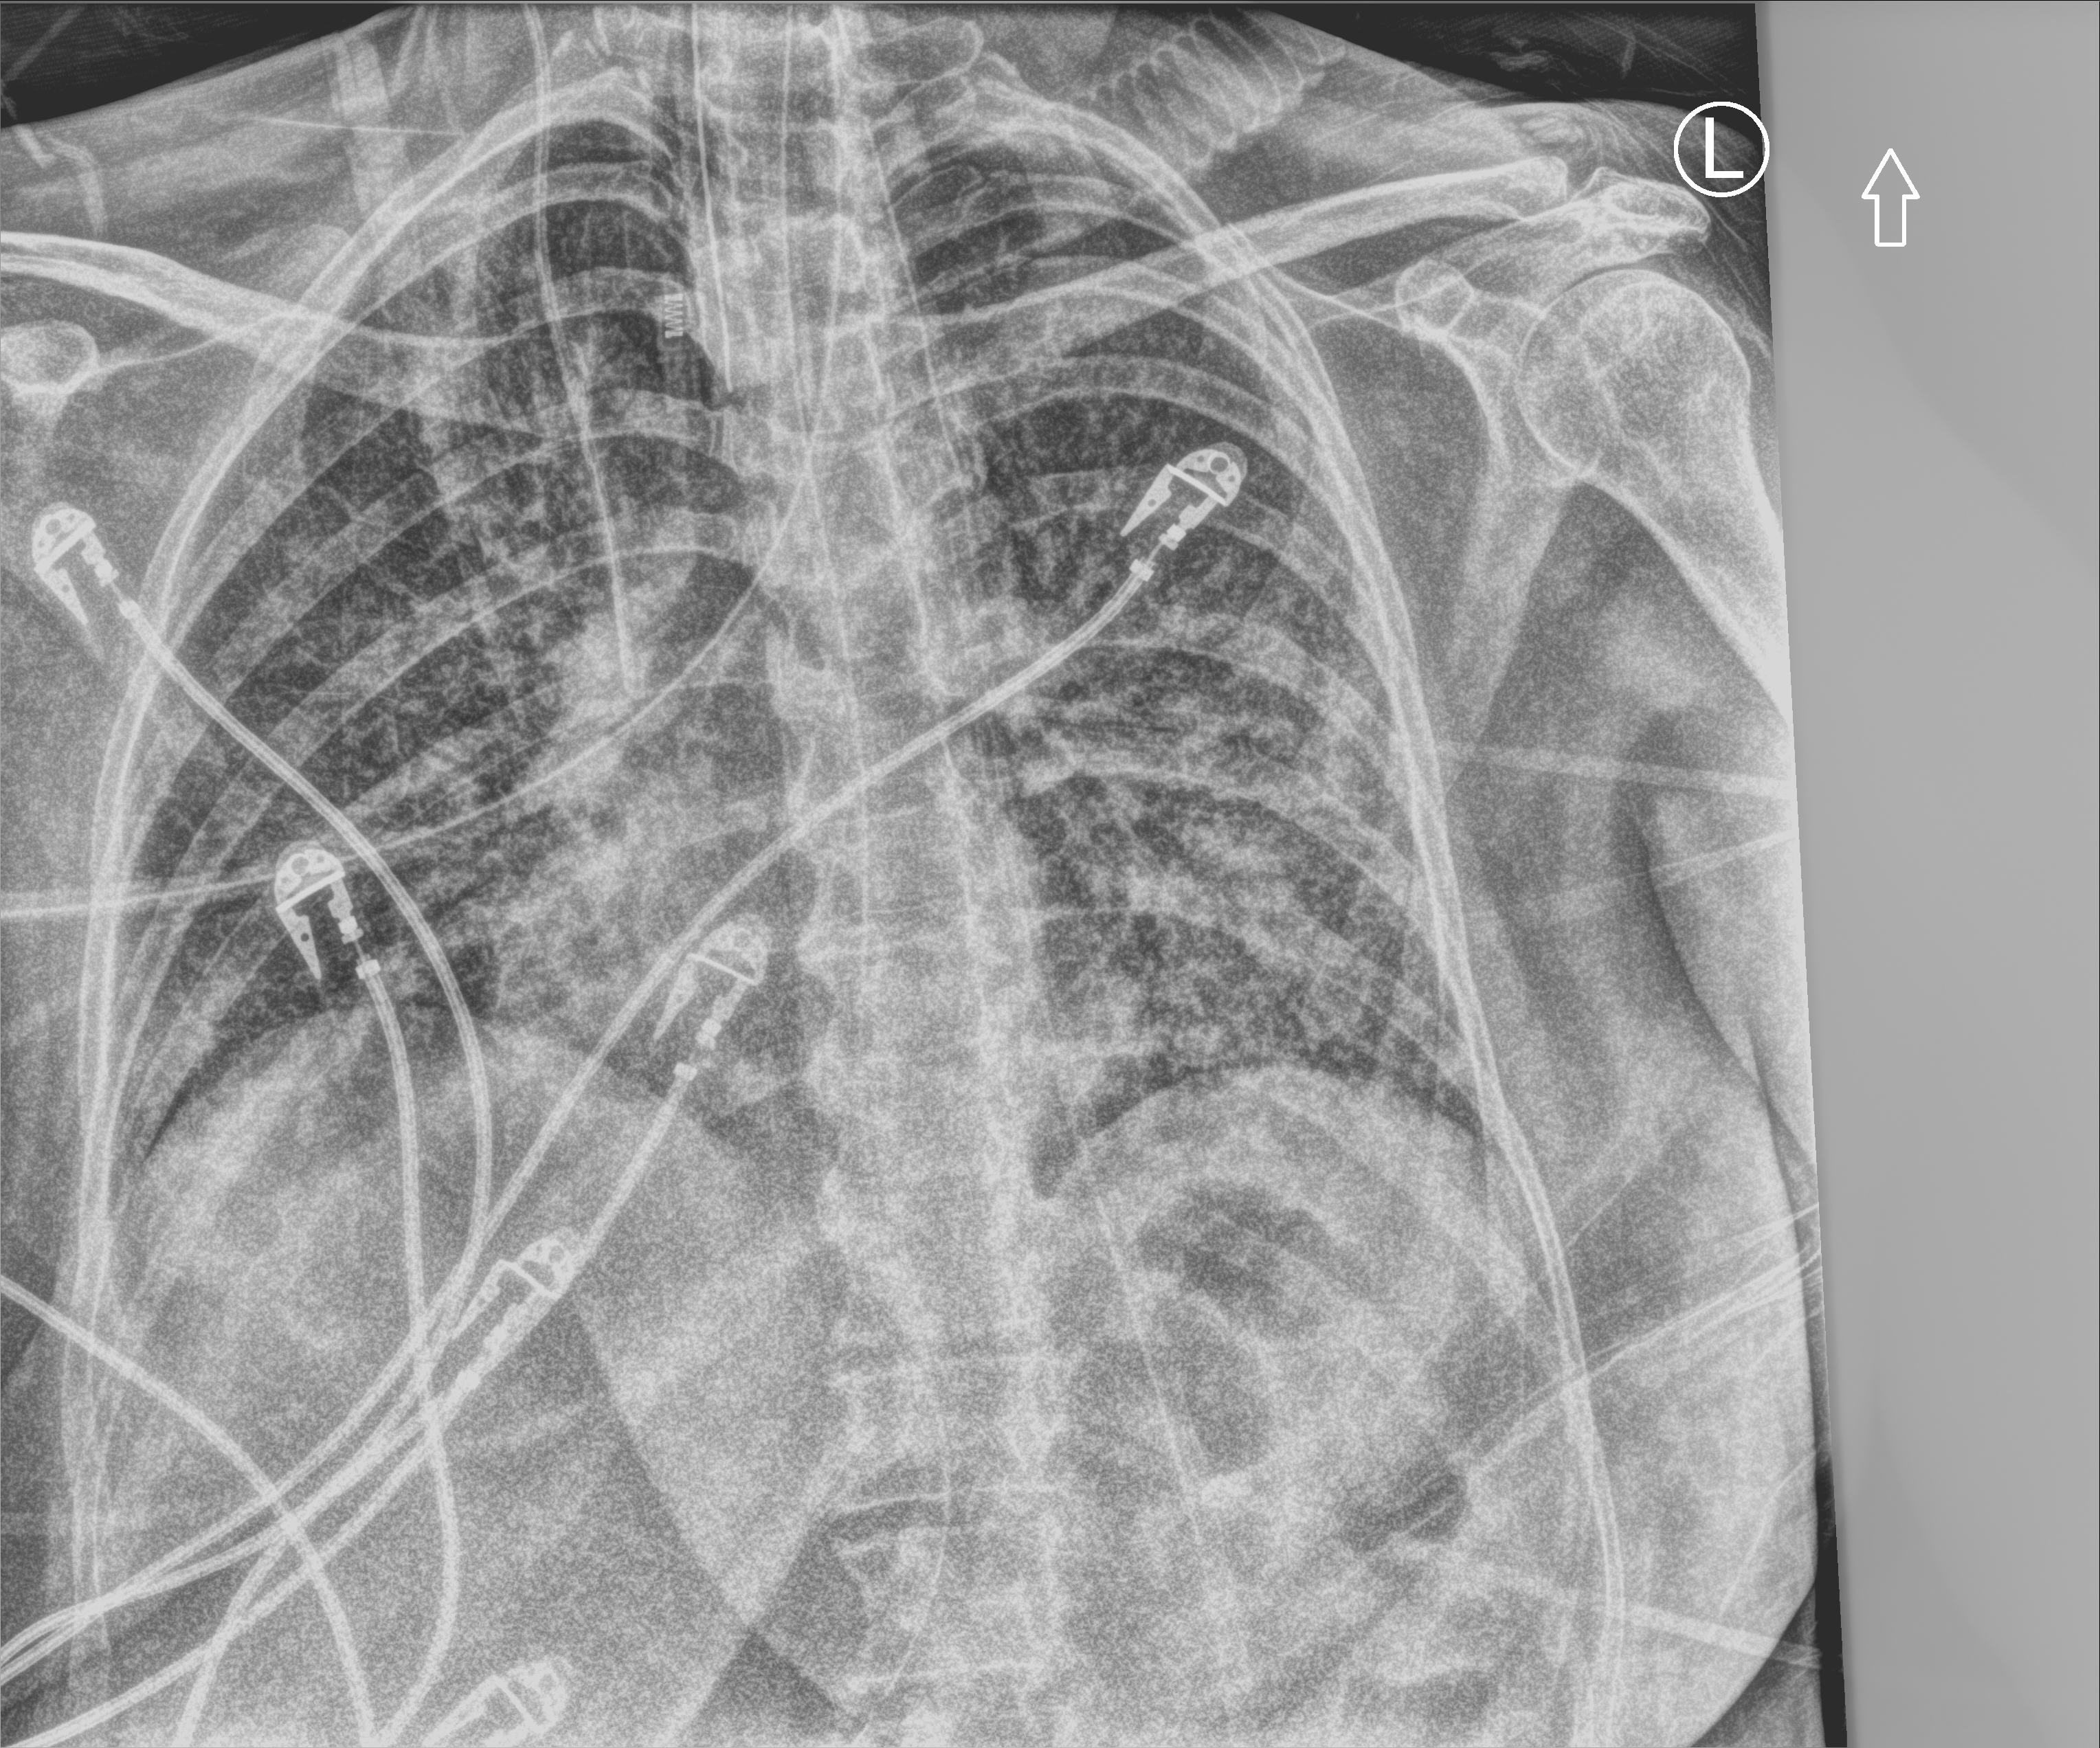
Bedside chest radiograph (computed radiography), anteroposterior (AP) projection. Patient hospitalised with COVID-19; female, aged 60–74 years.
Admission-level facts for this patient (not findings on this image; timing relative to this image not recorded): admitted to intensive care during this hospital stay: yes; mechanically ventilated during this hospital stay: yes; chronic kidney disease (admission record): no.